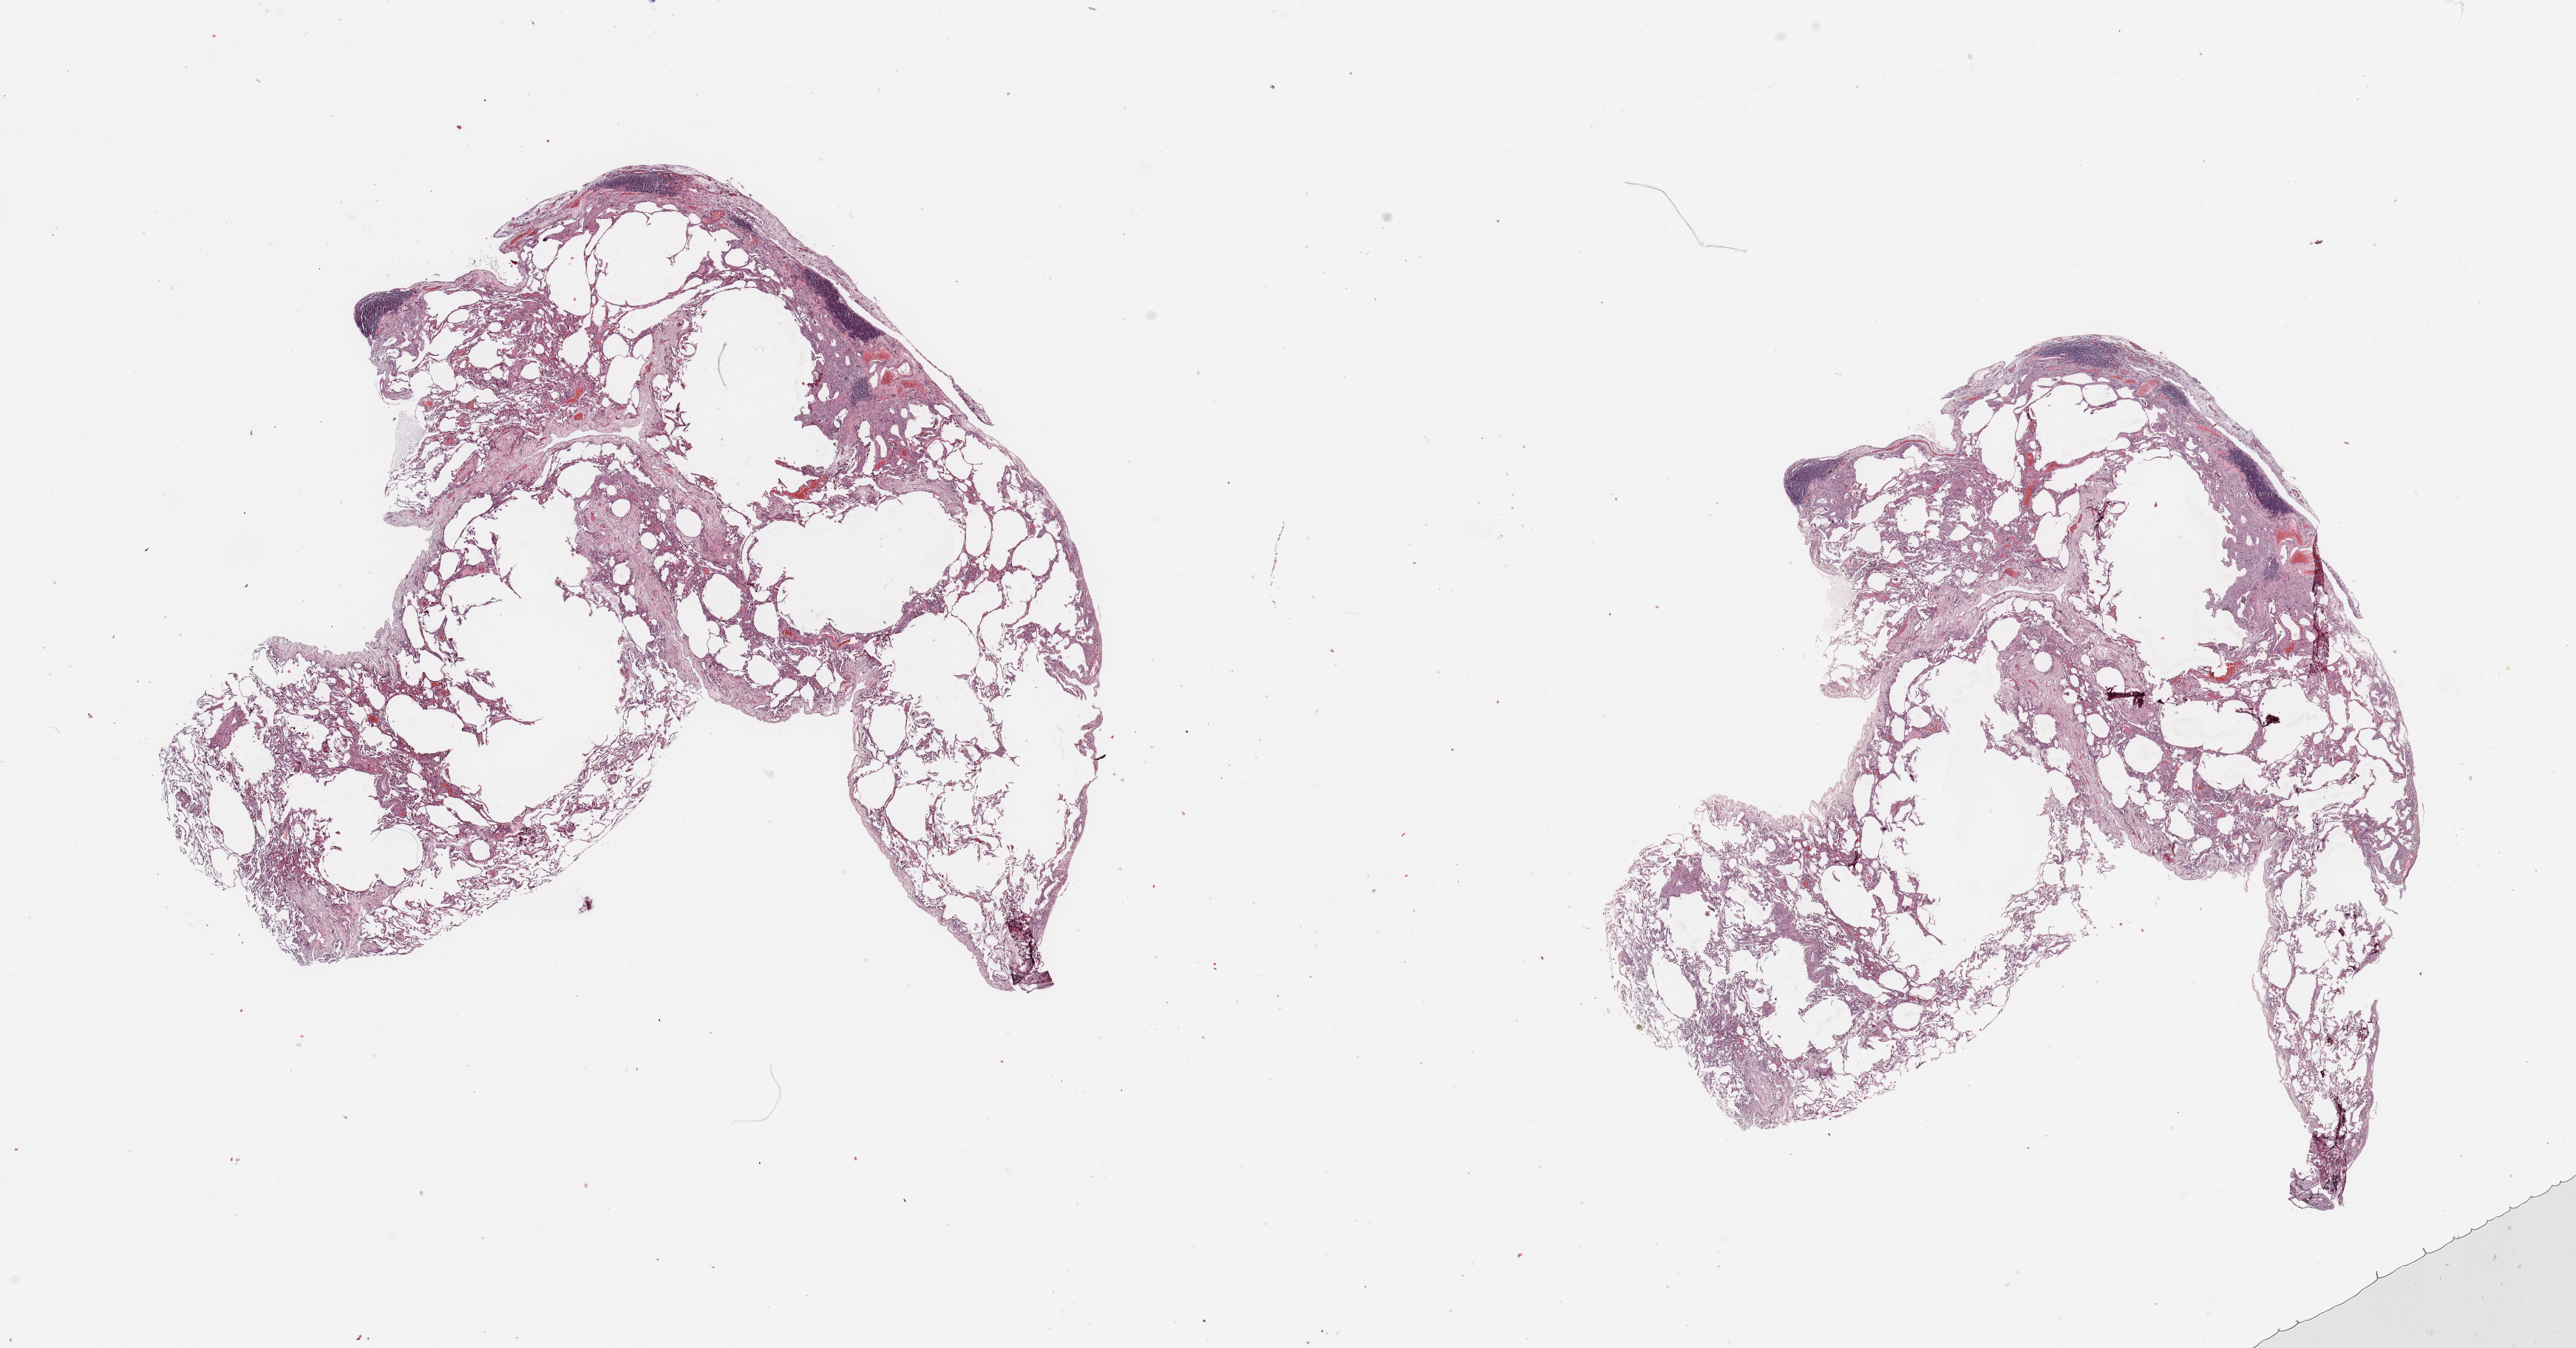
Digitized H&E tissue section (whole slide), a low-resolution overview of the entire scanned area, about 27.6 x 14.4 mm; normal (non-tumour) tissue sample, lung. 64-year-old male patient.
This section: normal (non-tumour) tissue from the same patient. Patient diagnosis: Adenocarcinoma, NOS.